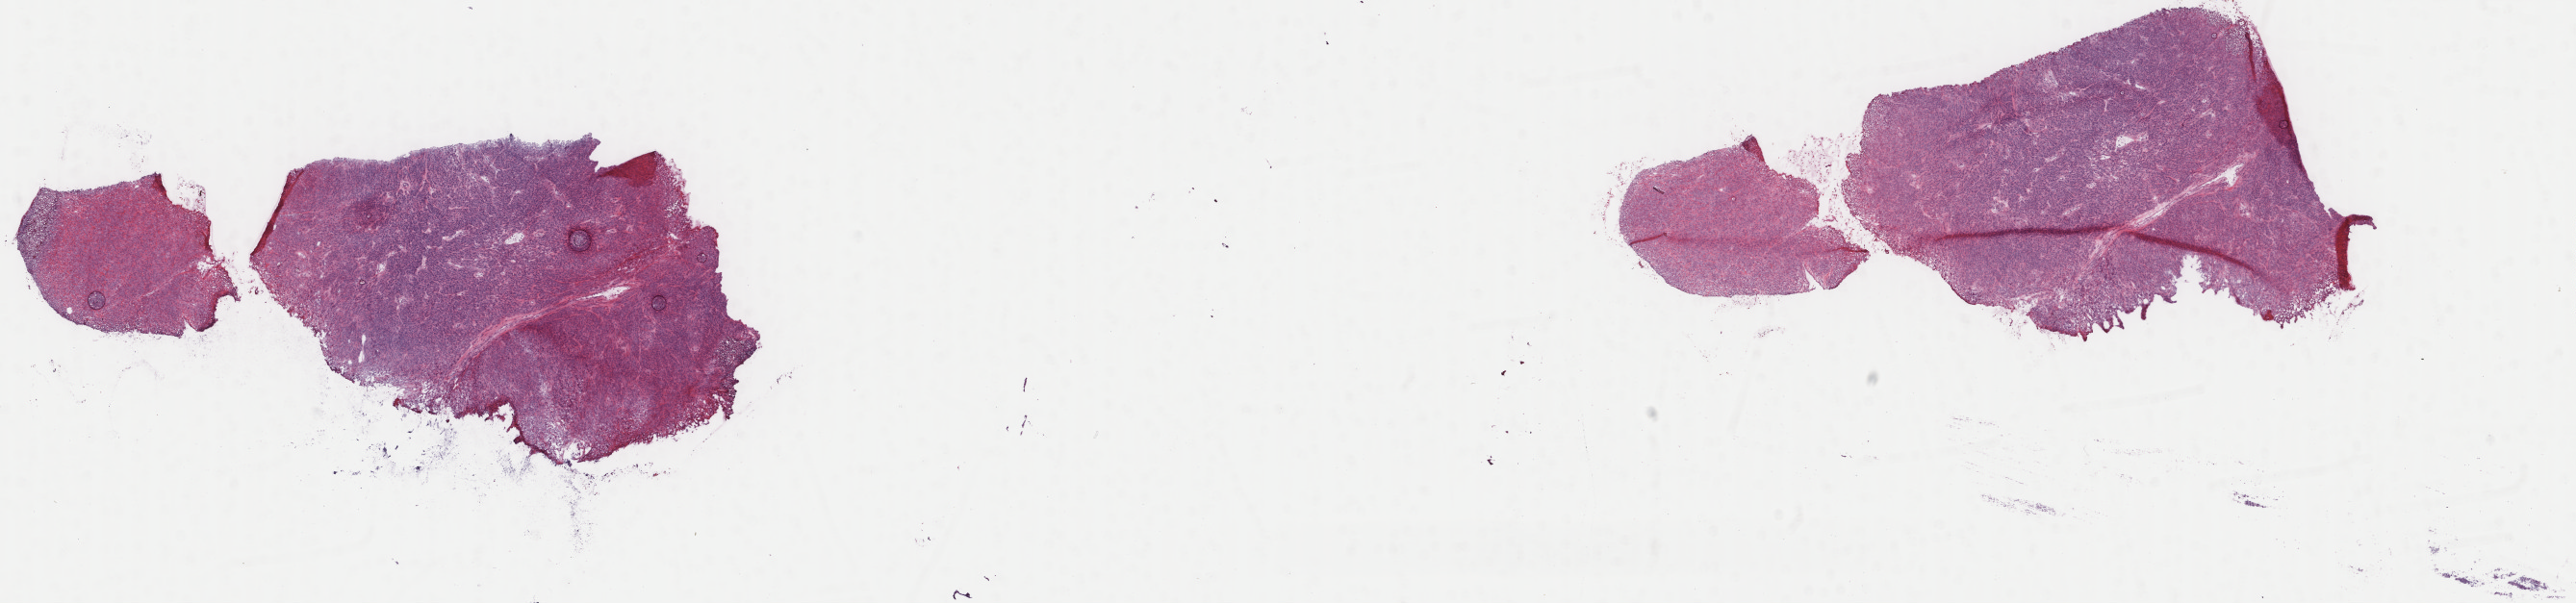
Whole-slide histology image, H&E-stained — low-resolution overview of the scanned area, about 21.2 x 5.0 mm; frozen section from the top of the tissue portion; uterus, primary tumour sample. Female, age 69 years at initial diagnosis. Slide review estimates, as recorded: tumour cells 100%, tumour nuclei 80%, normal cells 0%, stromal cells 0%, necrosis 0%. Inflammatory infiltration, as recorded: lymphocyte infiltration 1%, monocyte infiltration 0%, neutrophil infiltration 0%.
Histologic diagnosis: Leiomyosarcoma, NOS.